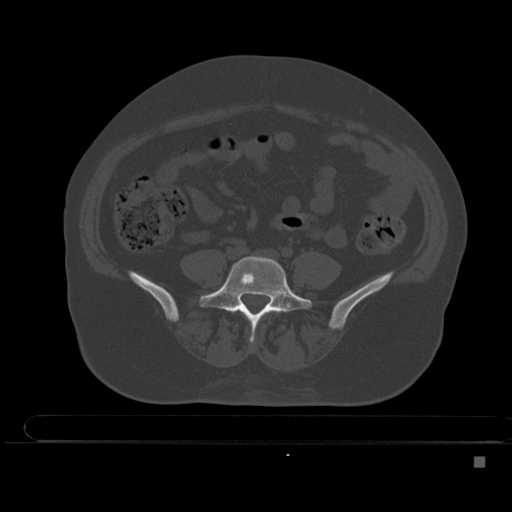
CT including the spine, one axial slice. Position 113 of 495 along the scan axis. Bone window (W 1800 / L 400 HU). 1.5 mm slice thickness. 512 × 512 image matrix, field of view 404 × 404 mm. Female patient, age 33 years. Case-level facts recorded for this patient, not image findings: primary cancer: breast; vertebrae with lytic lesions (as recorded): T1.
Structures marked on this image (semi-automatically segmented with operator editing):
- L4 vertebra: bounding box [x1, y1, x2, y2] px = [271, 310, 274, 312]
- L5 vertebra: [199, 256, 313, 341]